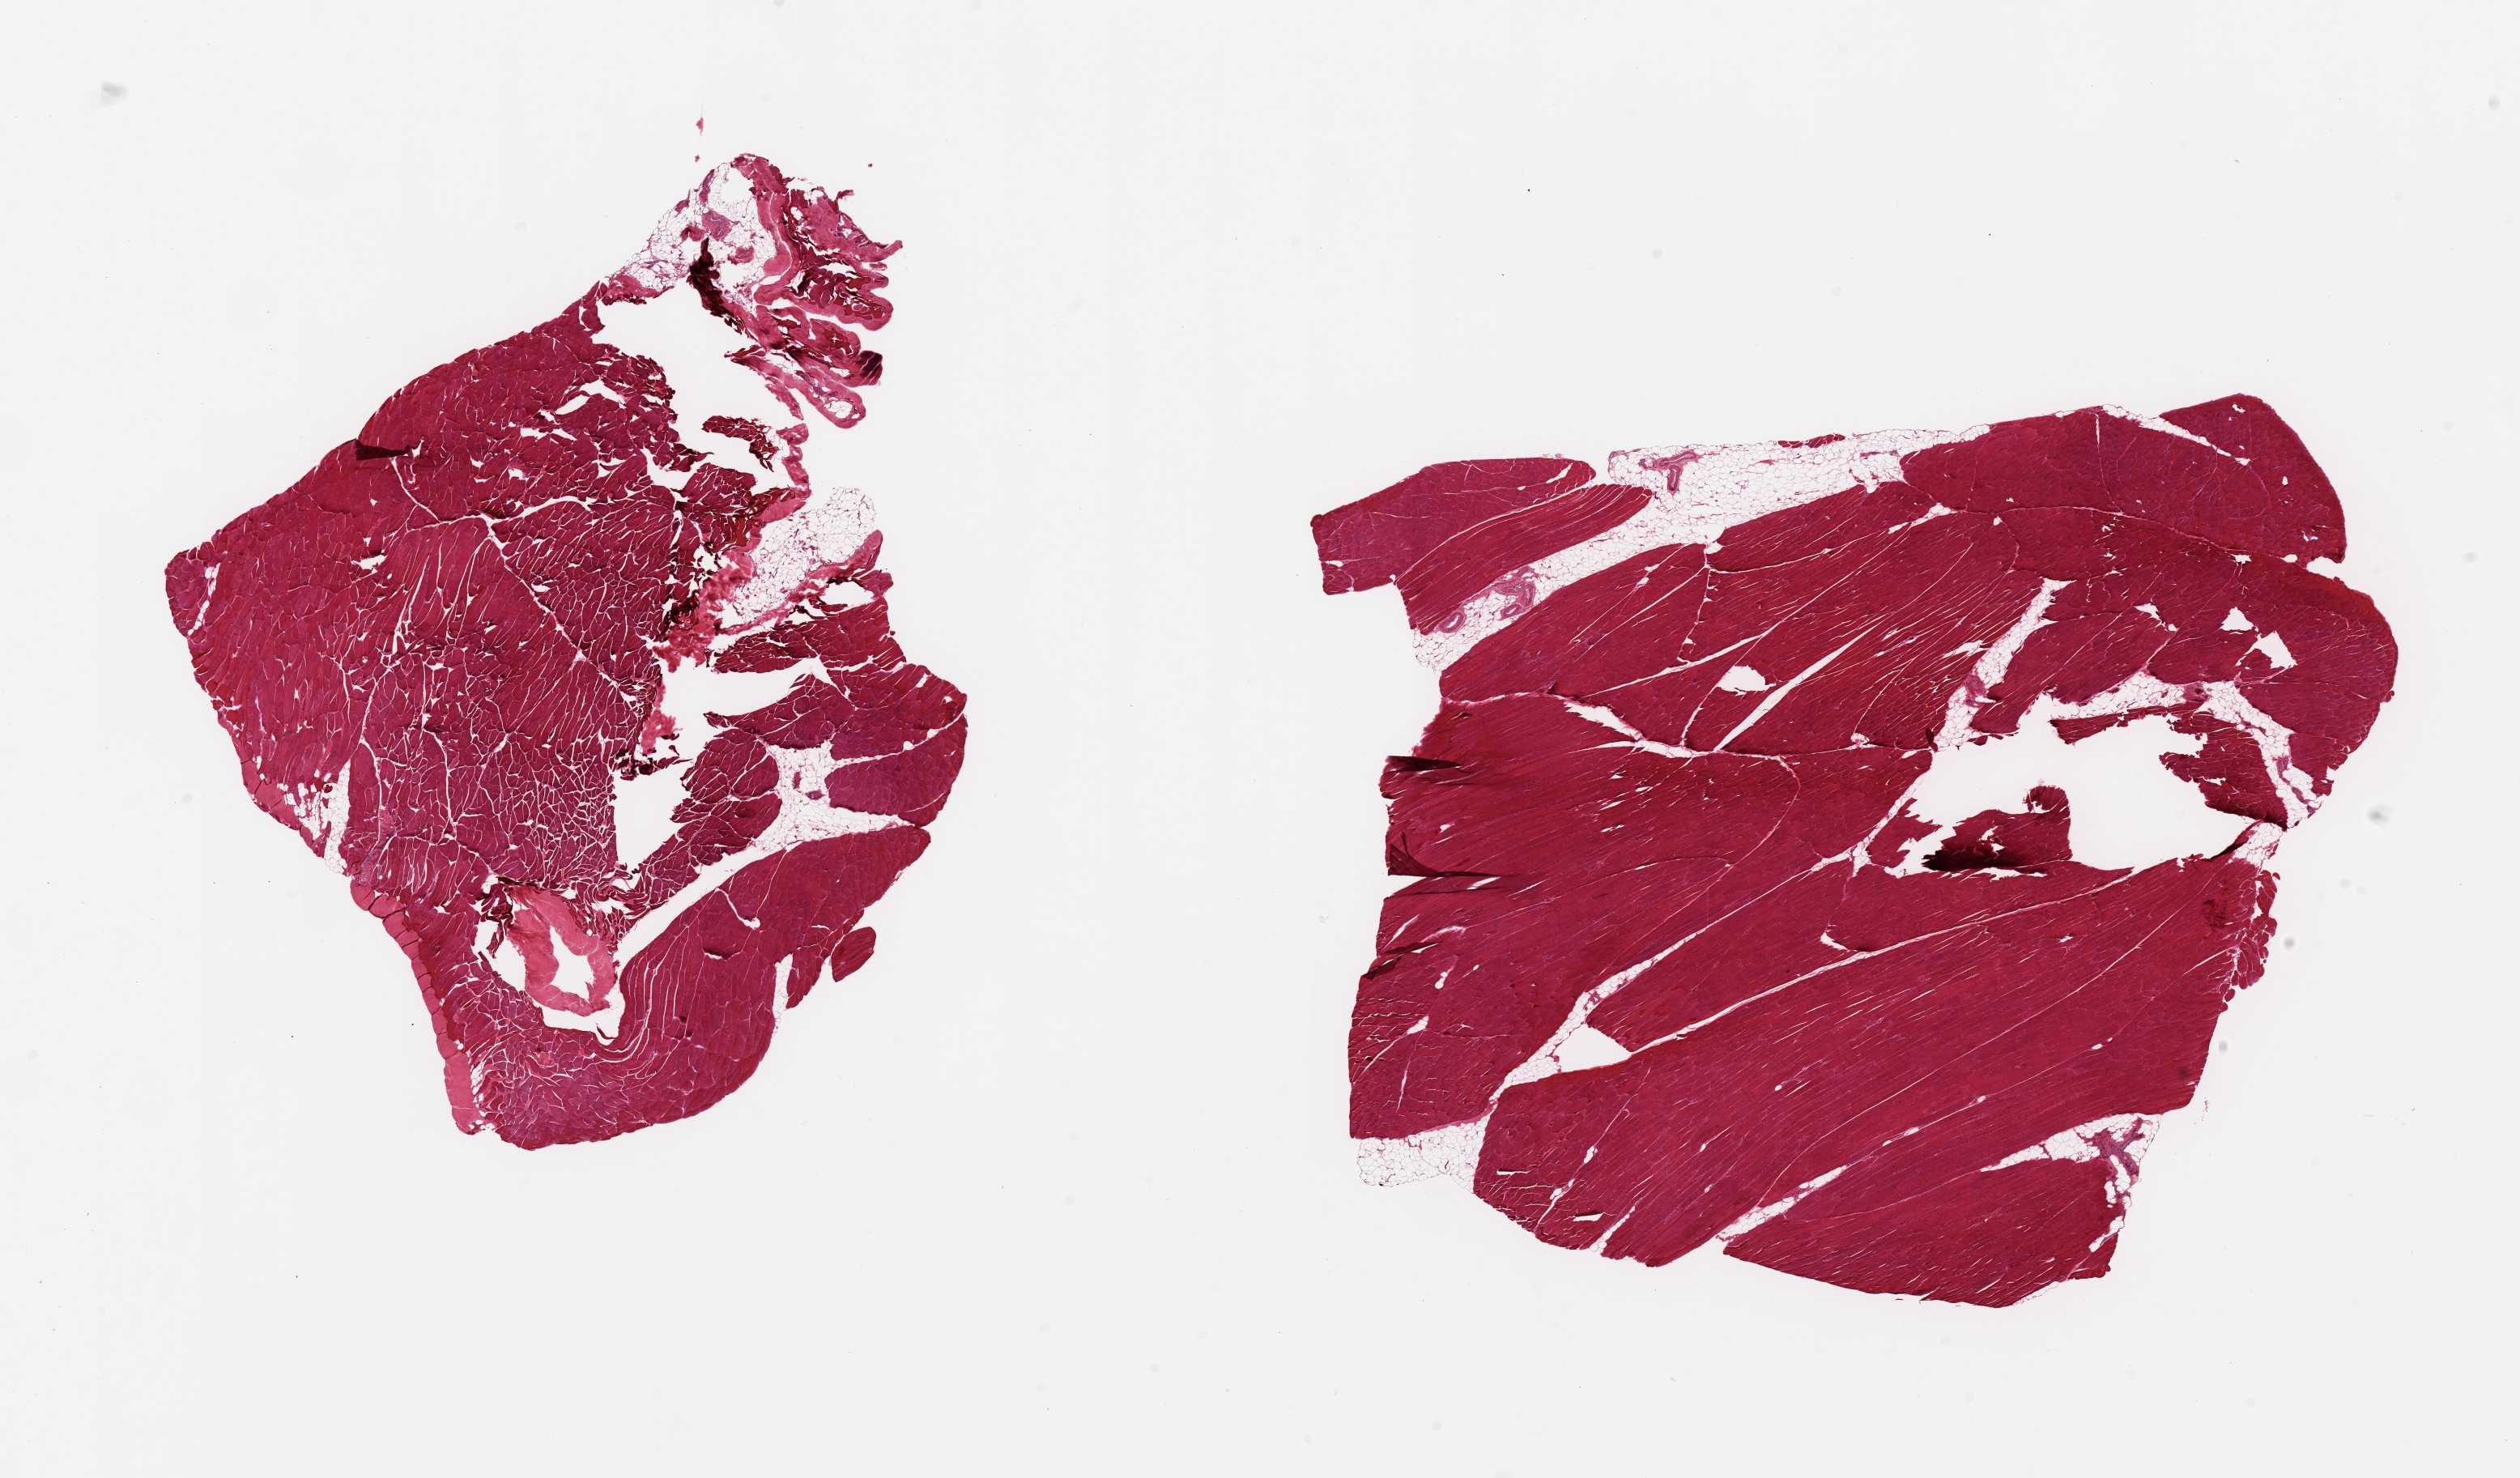
Whole-slide image, haematoxylin and eosin stain, brightfield, low-resolution overview of the scanned area, about 24.6 x 14.4 mm. PAXgene-fixed, paraffin-embedded tissue. Sampled site (target tissue): skeletal muscle. Tissue donor sample. Donor: male.
- reviewer comment on this tissue sample: 2 pieces; 5% fat content